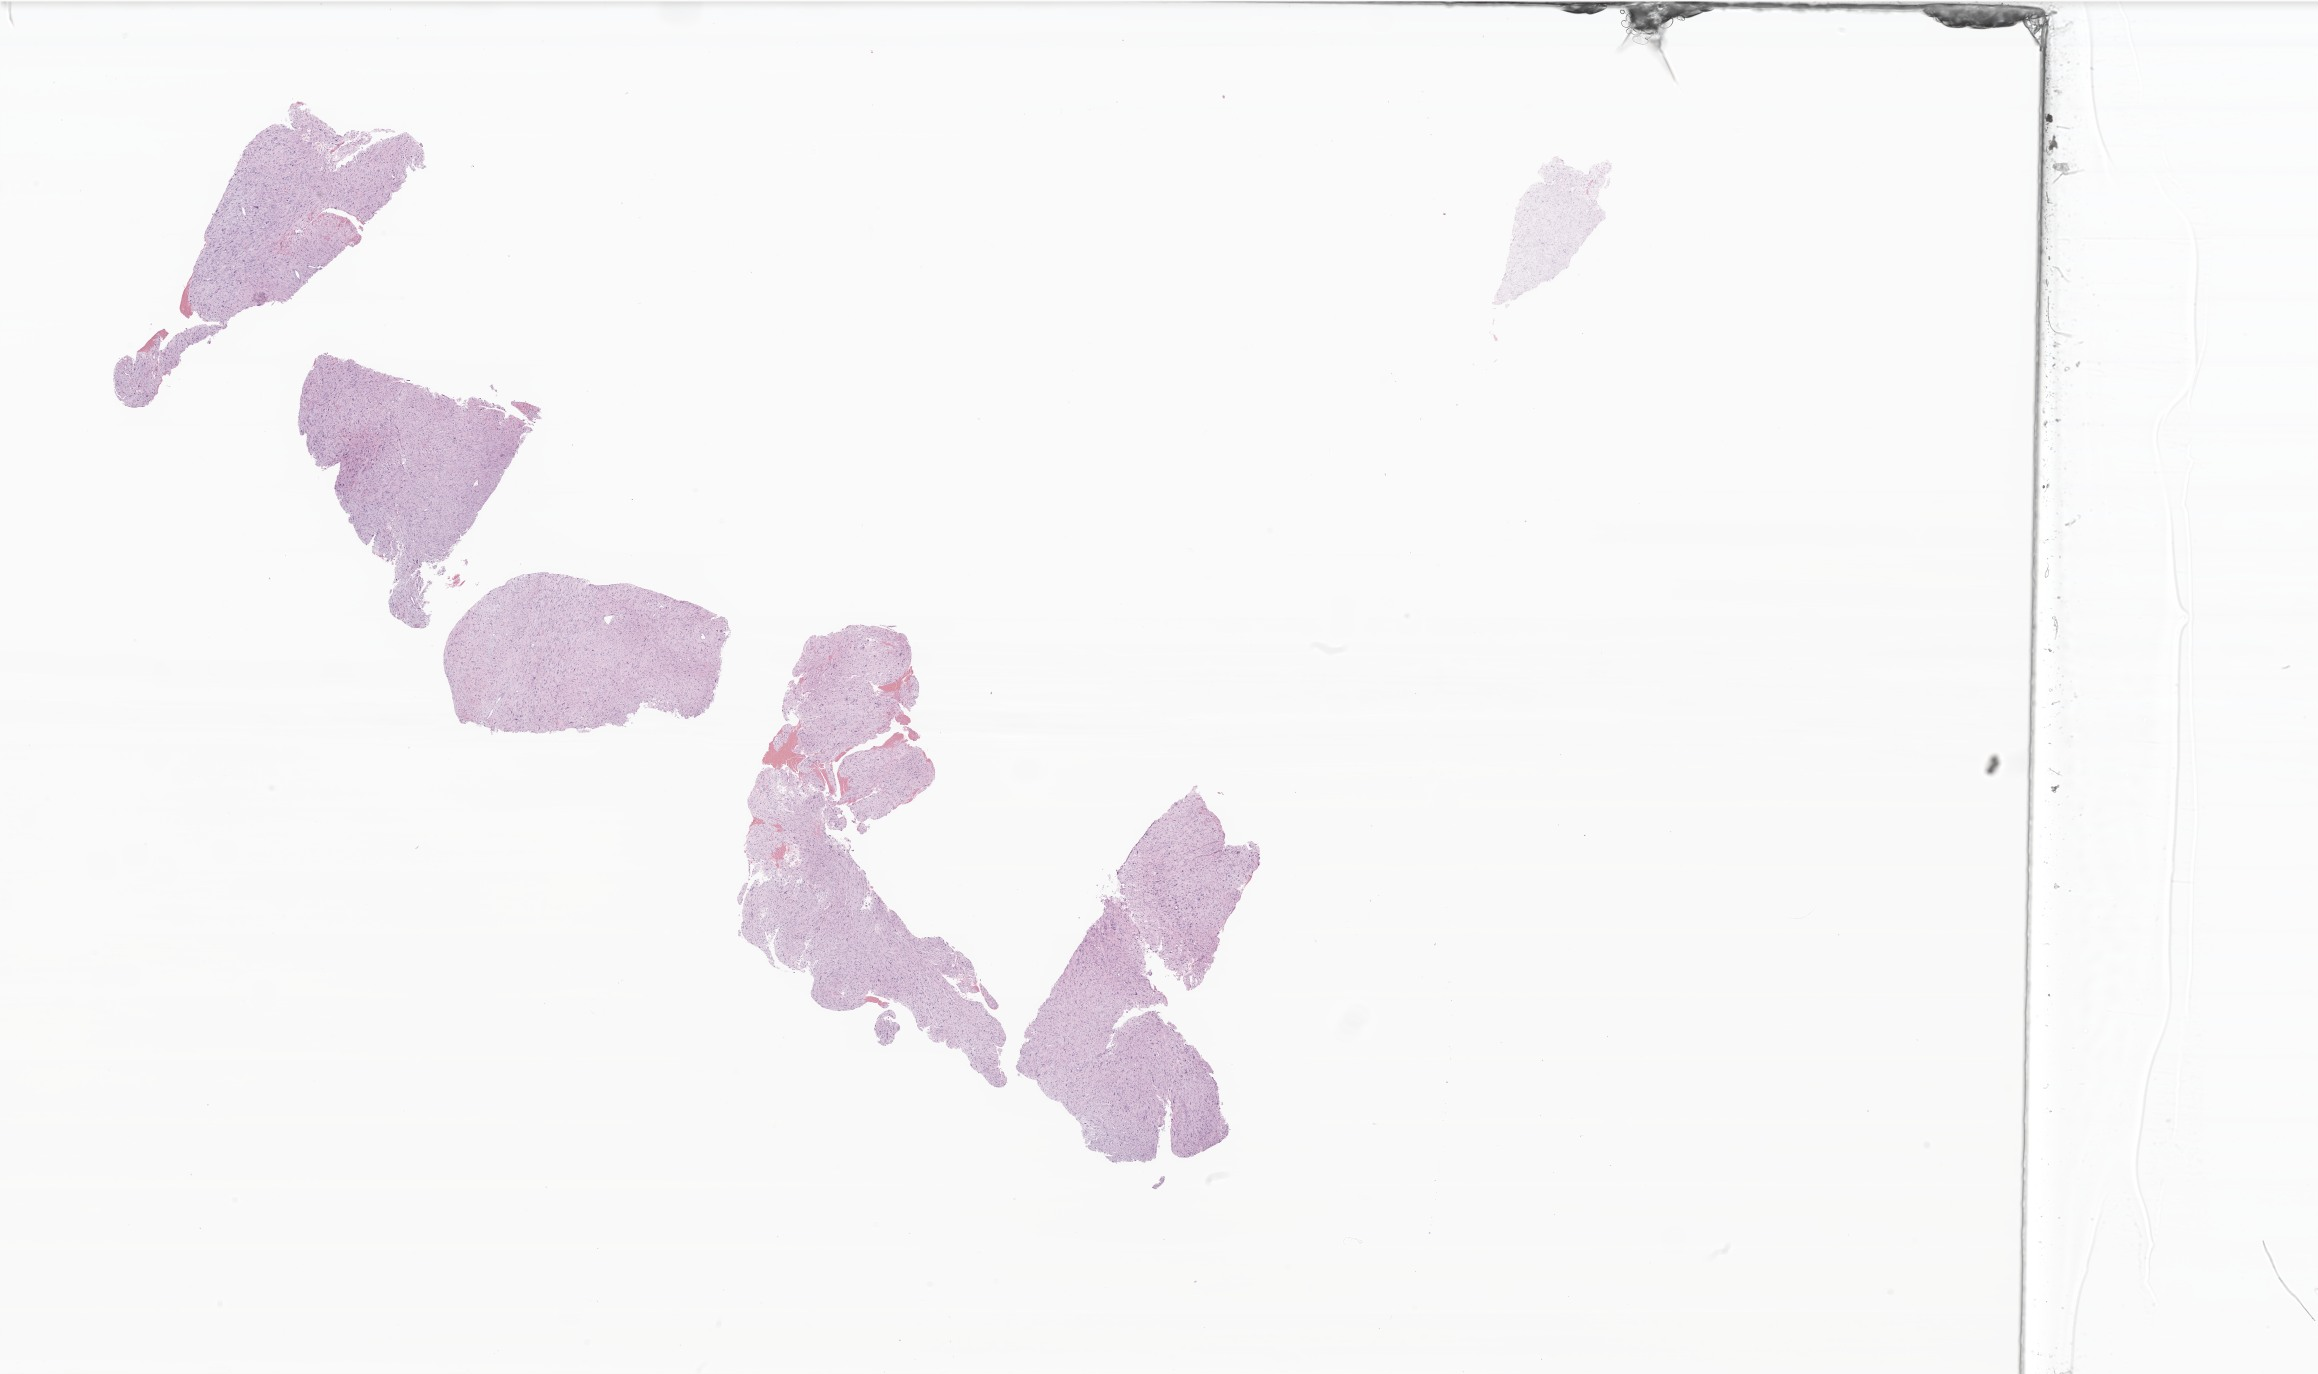
Whole-slide image, hematoxylin and eosin (H&E) stain of tumor tissue from the cranial and/or facial bone — shown as a low-resolution overview of the whole scanned area (about 39.1 x 23.2 mm); FFPE section. Female patient, age 103 months (8 years 7 months).
Recorded diagnosis: Spindle cell rhabdomyosarcoma.